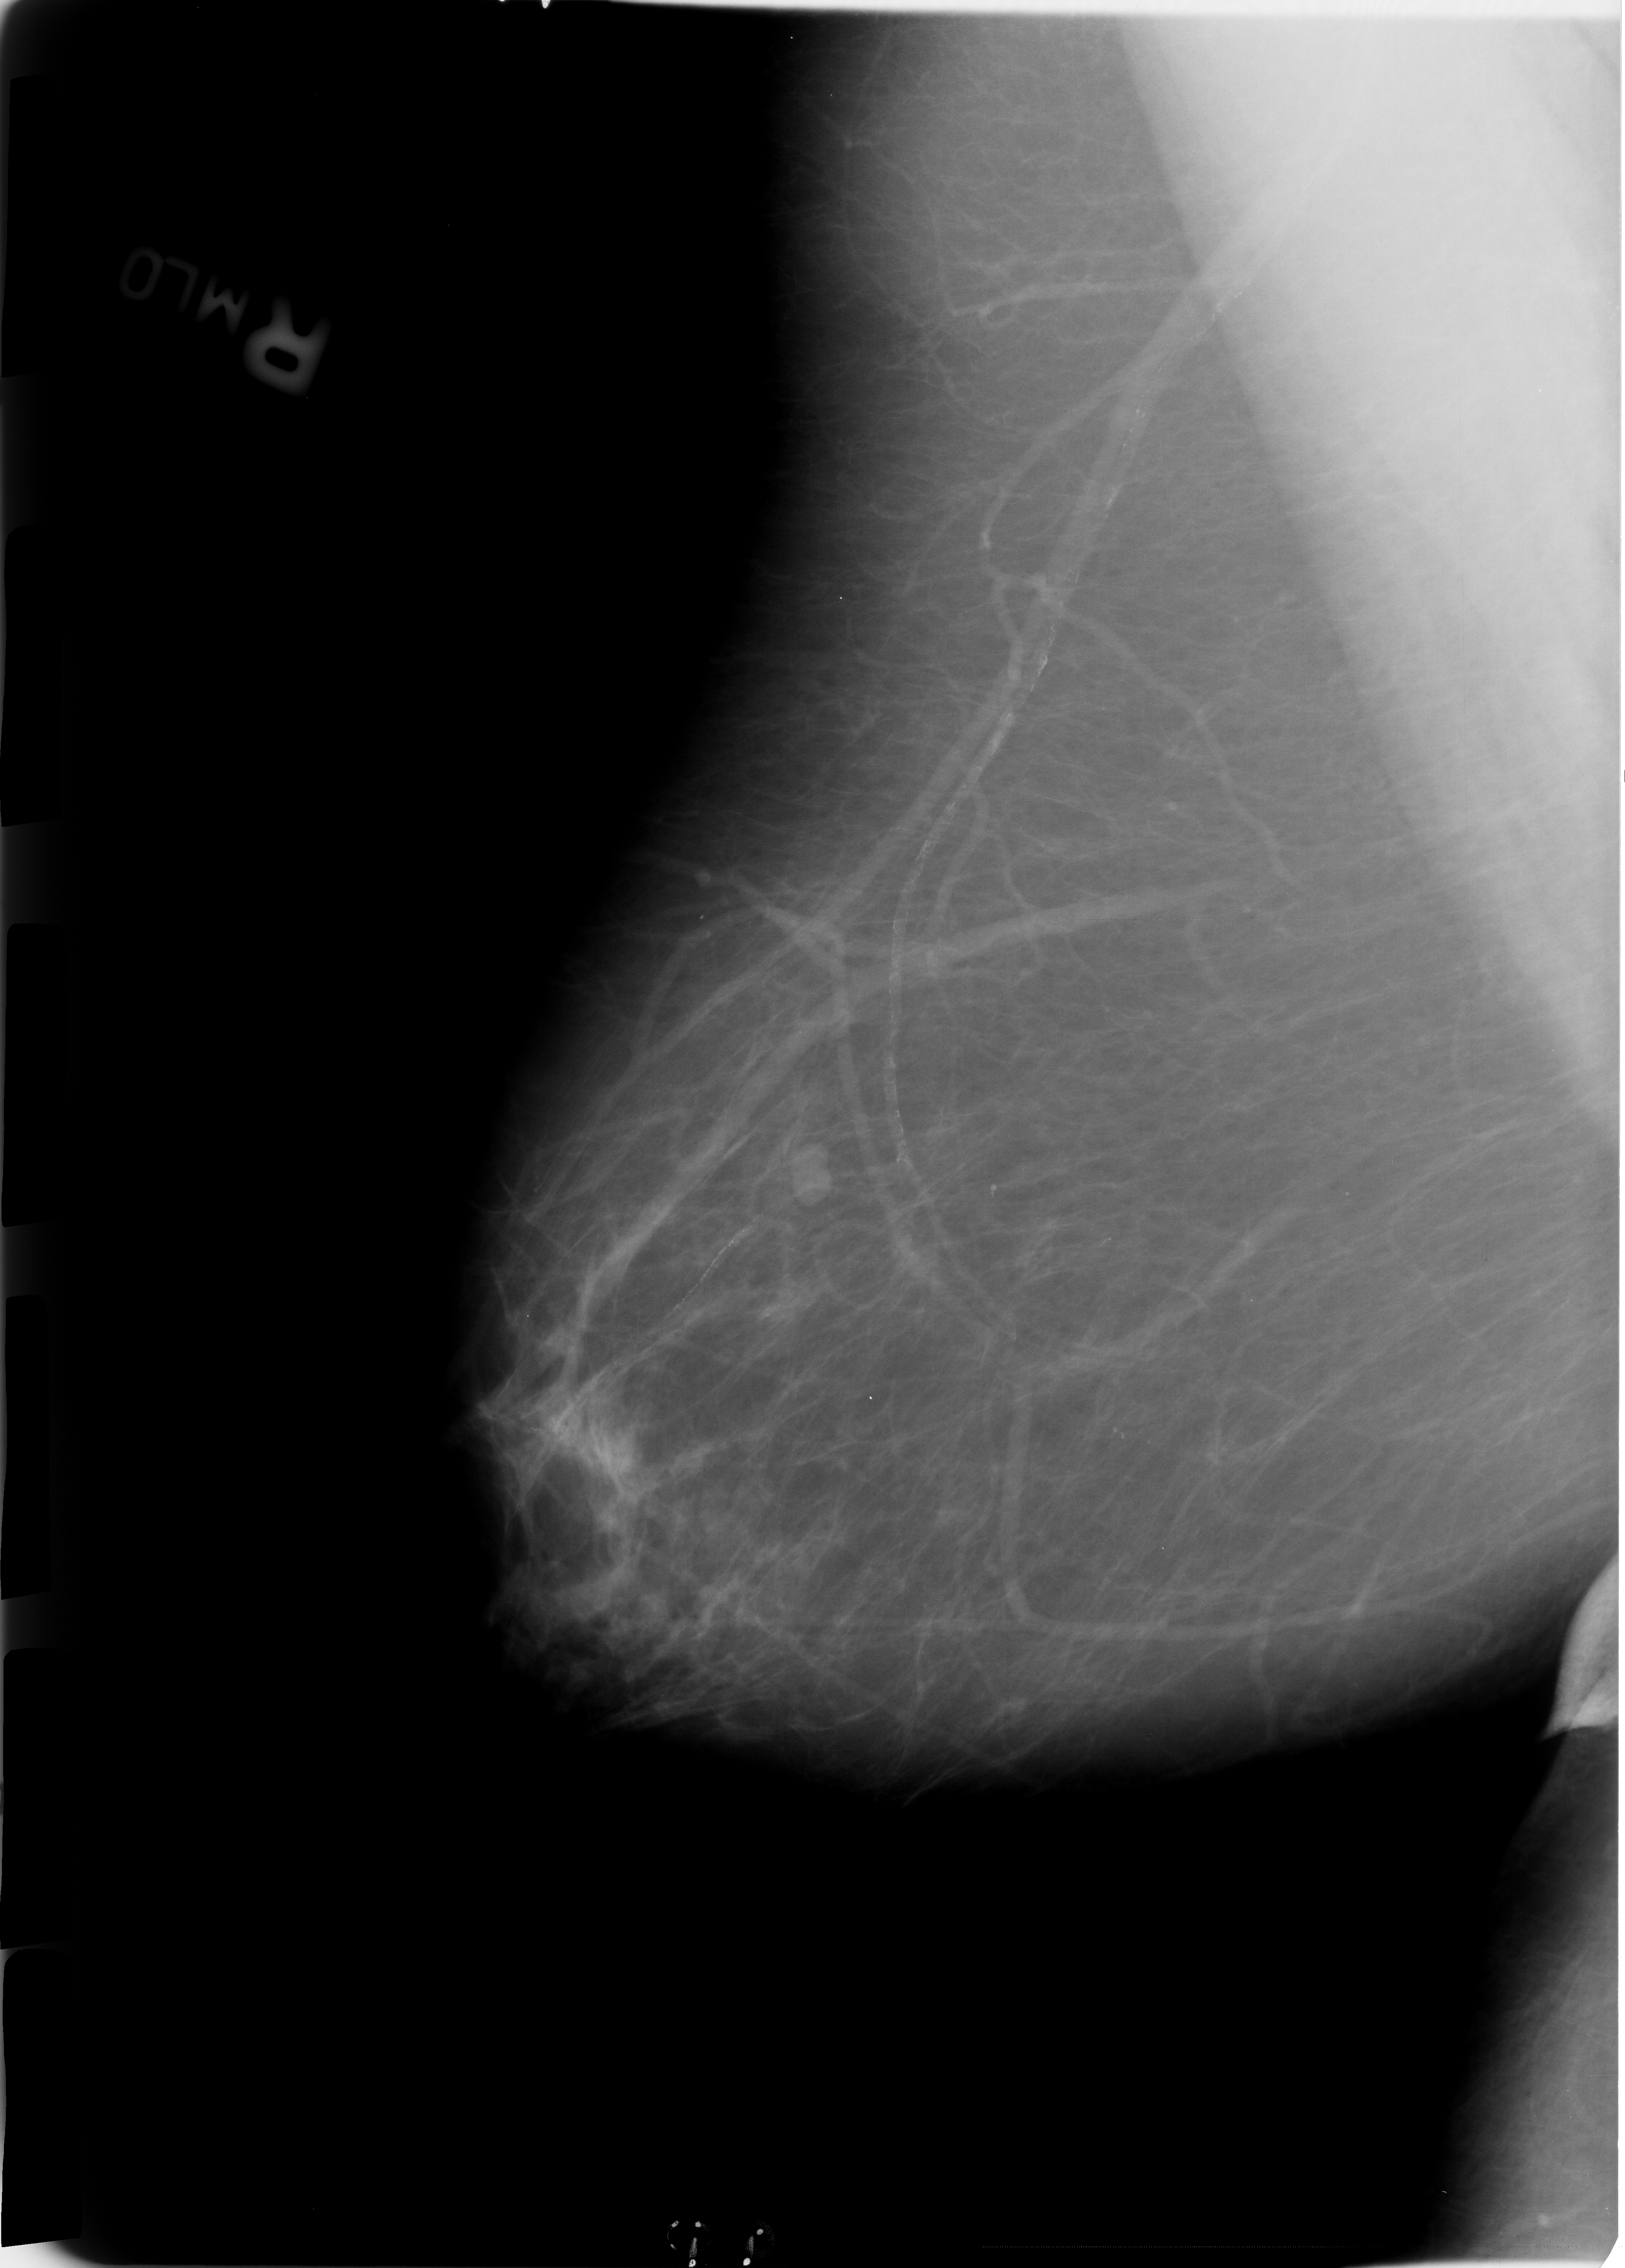
Digitized screen-film mammogram, right breast, MLO view, breast composition: scattered fibroglandular densities (BI-RADS density category 2 of 4).
Marked findings (only marked abnormalities are described; nothing is implied about the rest of the image): mass, shape lobulated / lymph node, margins circumscribed; BI-RADS assessment category 2; subtlety rating 4 on a 1 (subtle) to 5 (obvious) scale; benign; no additional work-up was recommended (benign without callback).